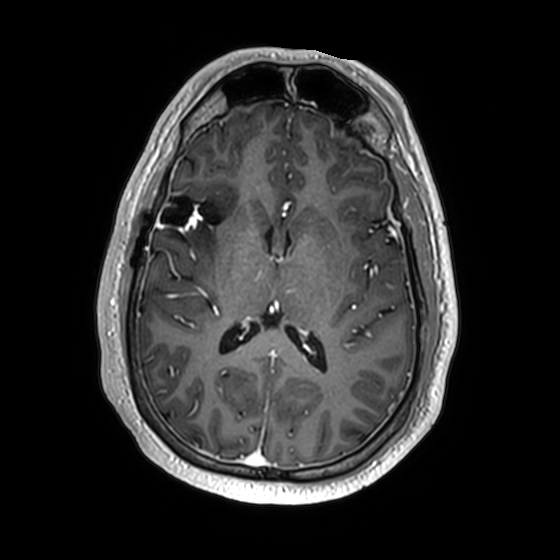
Brain MRI from a brain-tumour surgery series, one axial slice. Slice 84 of 174 in the series (ordered by position). T1-weighted post-contrast. 560 × 560 image matrix, field of view 256 × 256 mm. From the clinical record (not read from this slice): histopathology: Astrocytoma; WHO grade: 2; IDH mutation: yes; tumour location: Right Insular.
Annotated regions visible in this slice (expert manual segmentation):
- previous resection cavity: bounding box (x1, y1, x2, y2) in pixels: (160, 196, 219, 225)